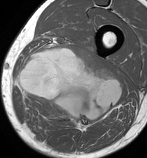
MRI of an extremity soft-tissue mass, one axial slice; position 47 of 86 along the scan axis; MR volume resampled by the dataset authors to the PET/CT grid (not the native acquisition matrix); 3.27 mm slice thickness; 147 × 158 image matrix. Male patient. From the clinical record (not read from this slice): histological type: undifferentiated pleomorphic liposarcoma; grade: high; site of the primary tumour: left thigh.
Annotated regions visible in this slice (expert contour drawn on MRI and transferred to this co-registered scan by the dataset authors):
- gross tumour volume including surrounding oedema: bounding box (x1, y1, x2, y2) in pixels: (14, 44, 124, 130)
- gross tumour volume (mass): (16, 44, 124, 130)